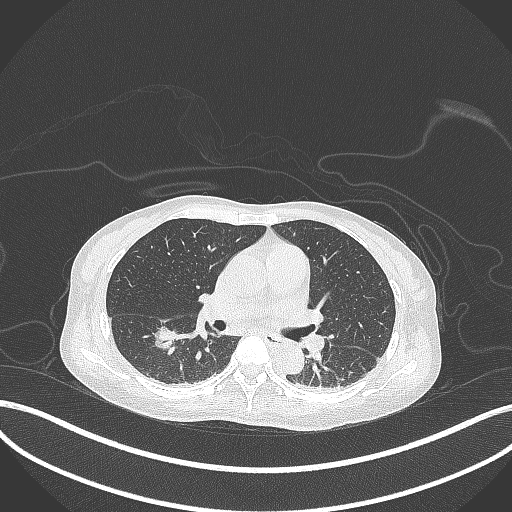
Chest CT, one axial slice. Slice 170 of 261 in the series (ordered by position). Lung window (W 1500 / L -600 HU). 512 × 512 image matrix, field of view 400 × 400 mm. Patient: female, 44 years. Case-level facts recorded for this patient, not image findings: clinical TNM (as recorded): T1c N0 M0.
Structures marked on this image (bounding box drawn by a radiologist):
- lung tumour (recorded histology: adenocarcinoma): bounding box [x1, y1, x2, y2] px = [152, 325, 179, 351]